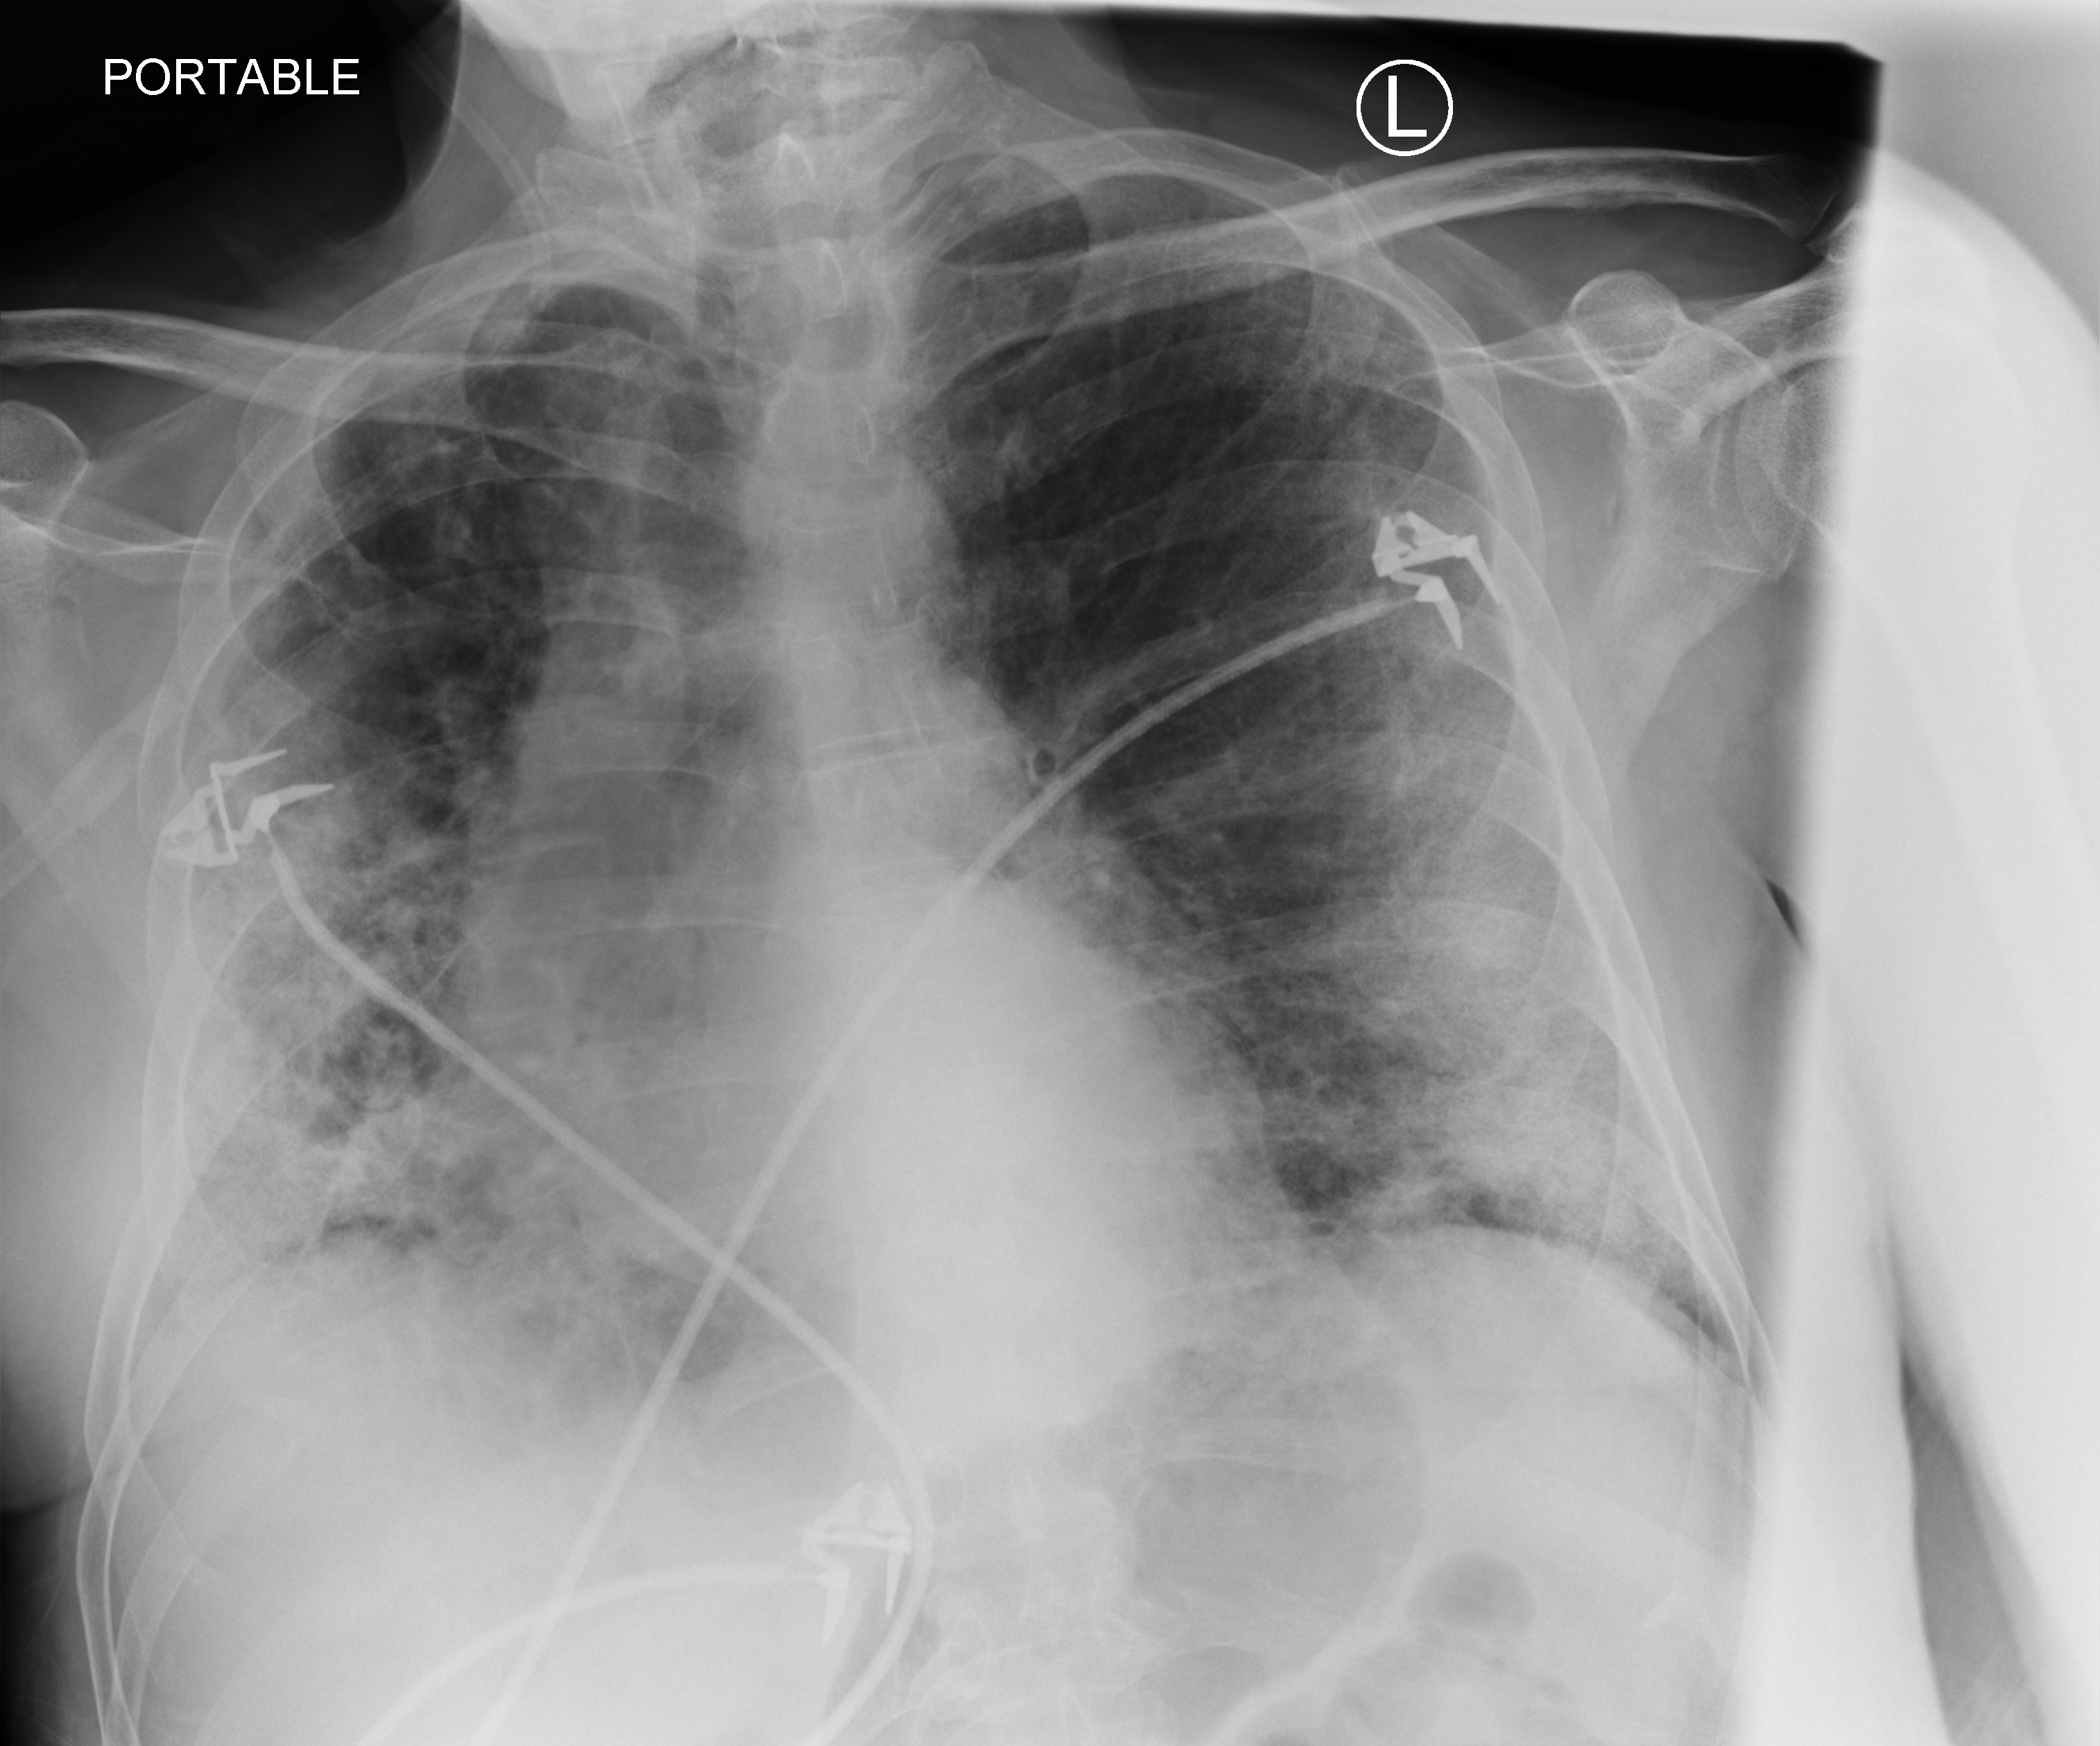
Chest X-ray (portable); anteroposterior (AP) projection. Male patient hospitalised with COVID-19, age 60–74 years.
From the hospital-stay record, not from the radiograph (when in the stay this image was taken is not recorded):
- mechanically ventilated during this hospital stay: no